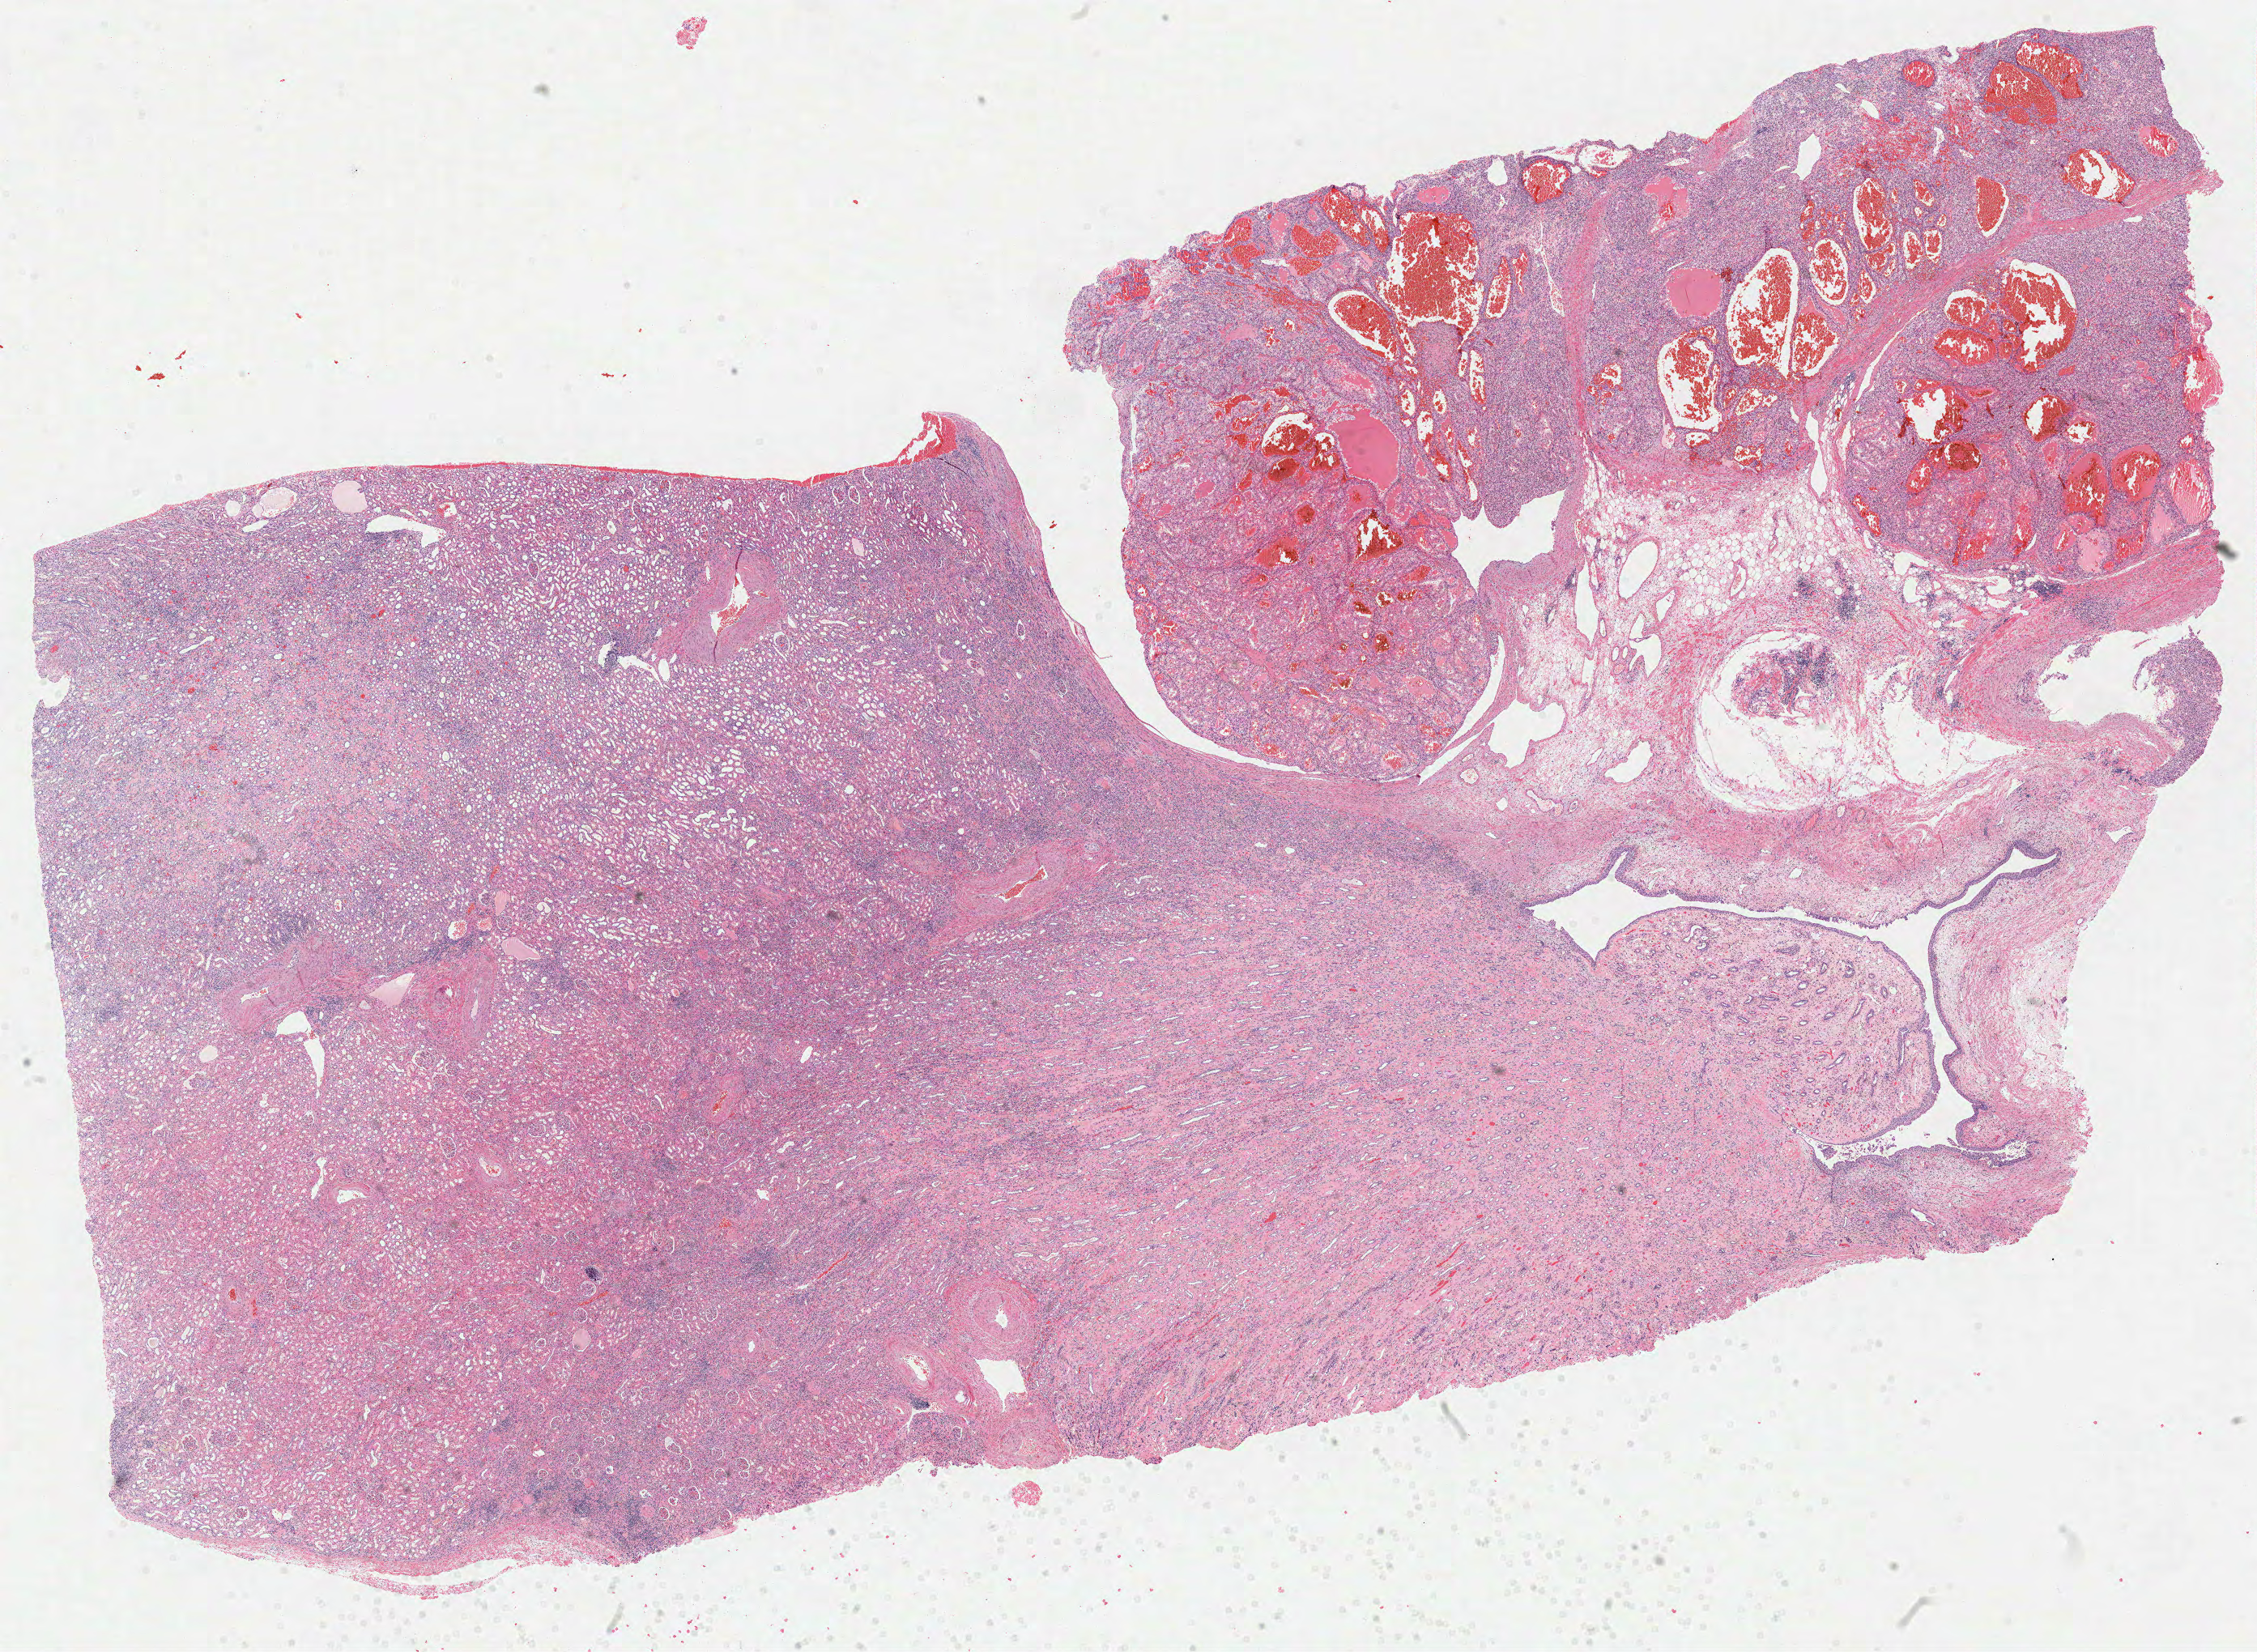
H&E whole-slide image — a low-resolution overview of the entire scanned area, about 22.5 x 16.5 mm; formalin-fixed paraffin-embedded (FFPE) diagnostic section; sample: primary tumour, kidney. Patient: male, age at initial diagnosis 81 years. Histologic grade: G3 (poorly differentiated).
AJCC pathologic stage: III. Pathologic diagnosis: Clear cell adenocarcinoma, NOS.